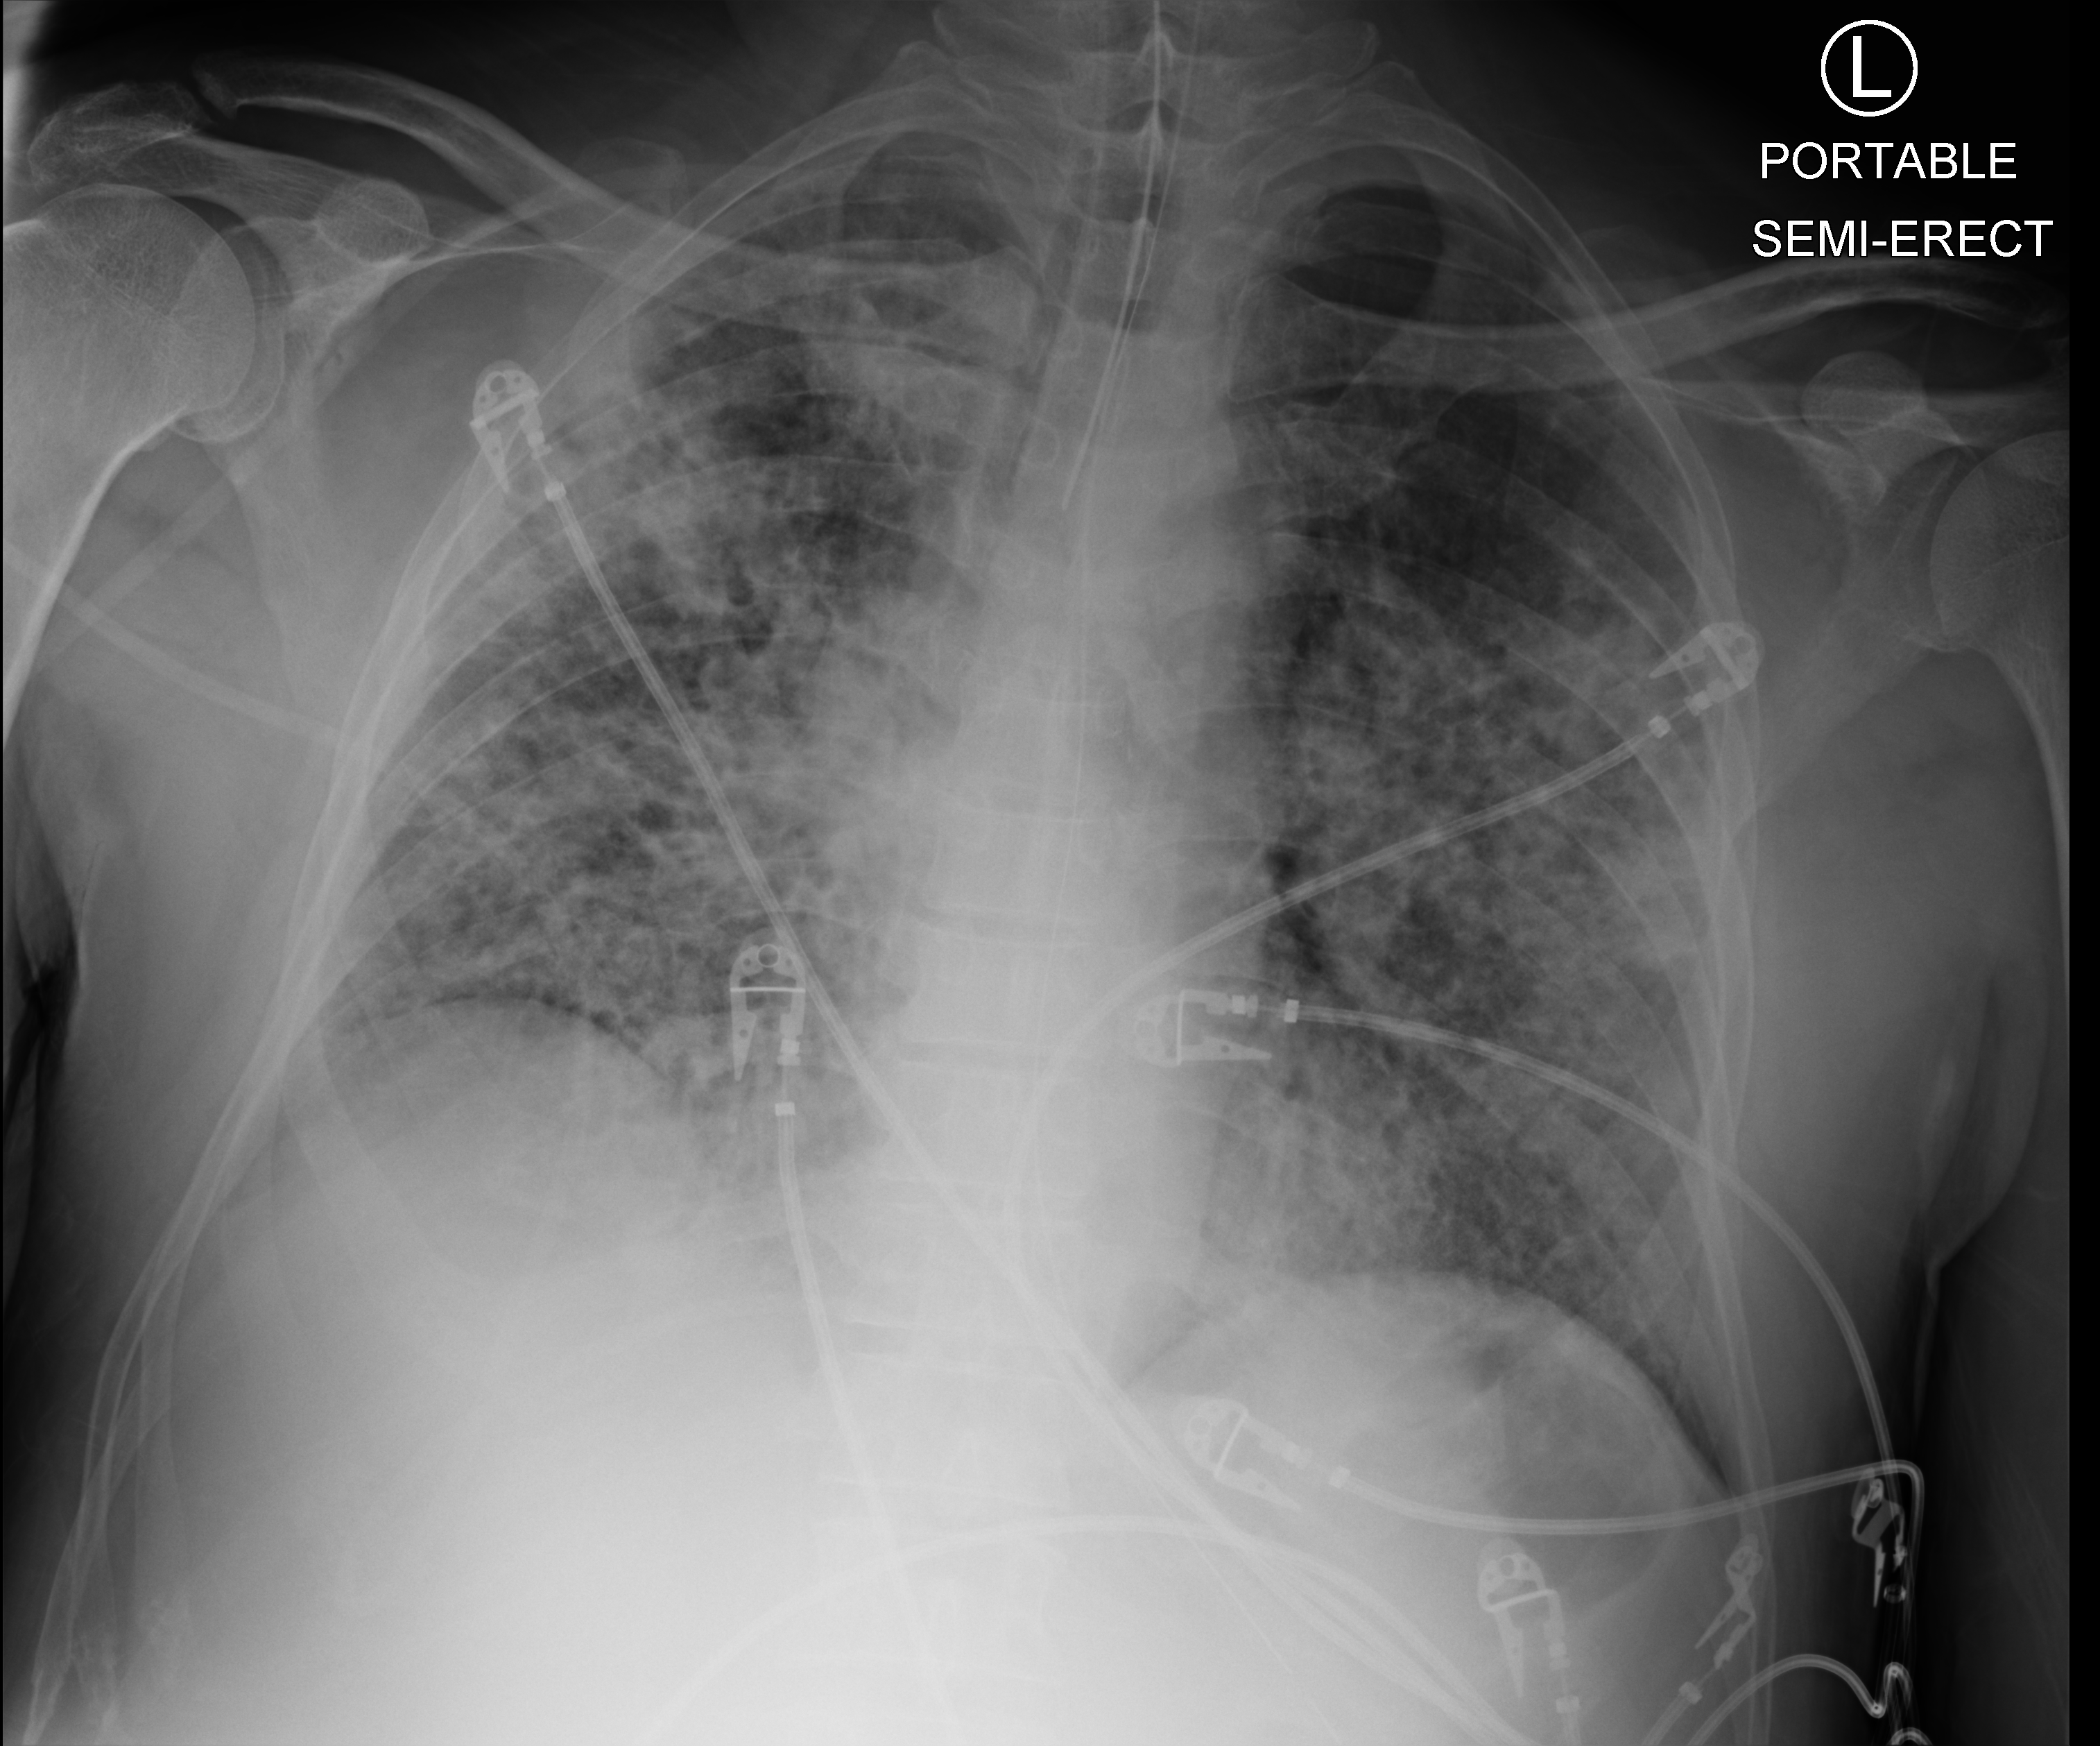
Portable chest radiograph. Patient hospitalised with COVID-19; male, aged 60–74 years.
Hospital-stay facts (about this admission, not read from this image; timing relative to this image not recorded): mechanically ventilated during this hospital stay: yes.